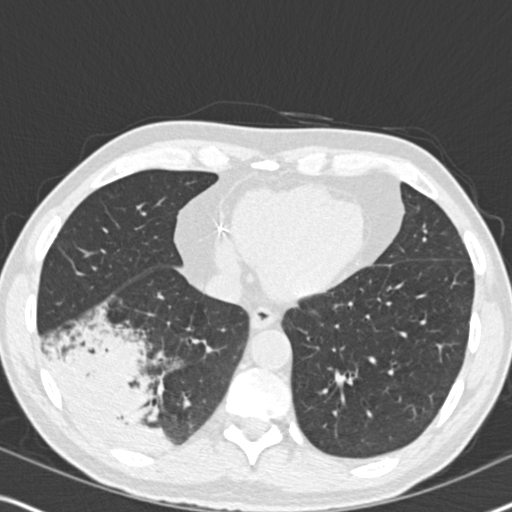
Chest CT (low-dose screening protocol), one axial image, second annual screen, lung window (W 1500 / L -600 HU), 2 mm slice thickness, standard (soft-tissue) reconstruction kernel (B30f). Male, age 61 years at enrolment.
Lesion marked by an expert reader, bounding box (x1, y1, x2, y2) in pixels: (37, 306, 186, 460). The exam's reader record, not a measurement of the box and not confirmed to be the same lesion: non-calcified nodule or mass ≥4 mm, right lower lobe, 90 × 80 mm, soft tissue attenuation, pre-existing on the prior screen: yes; interval growth: yes.